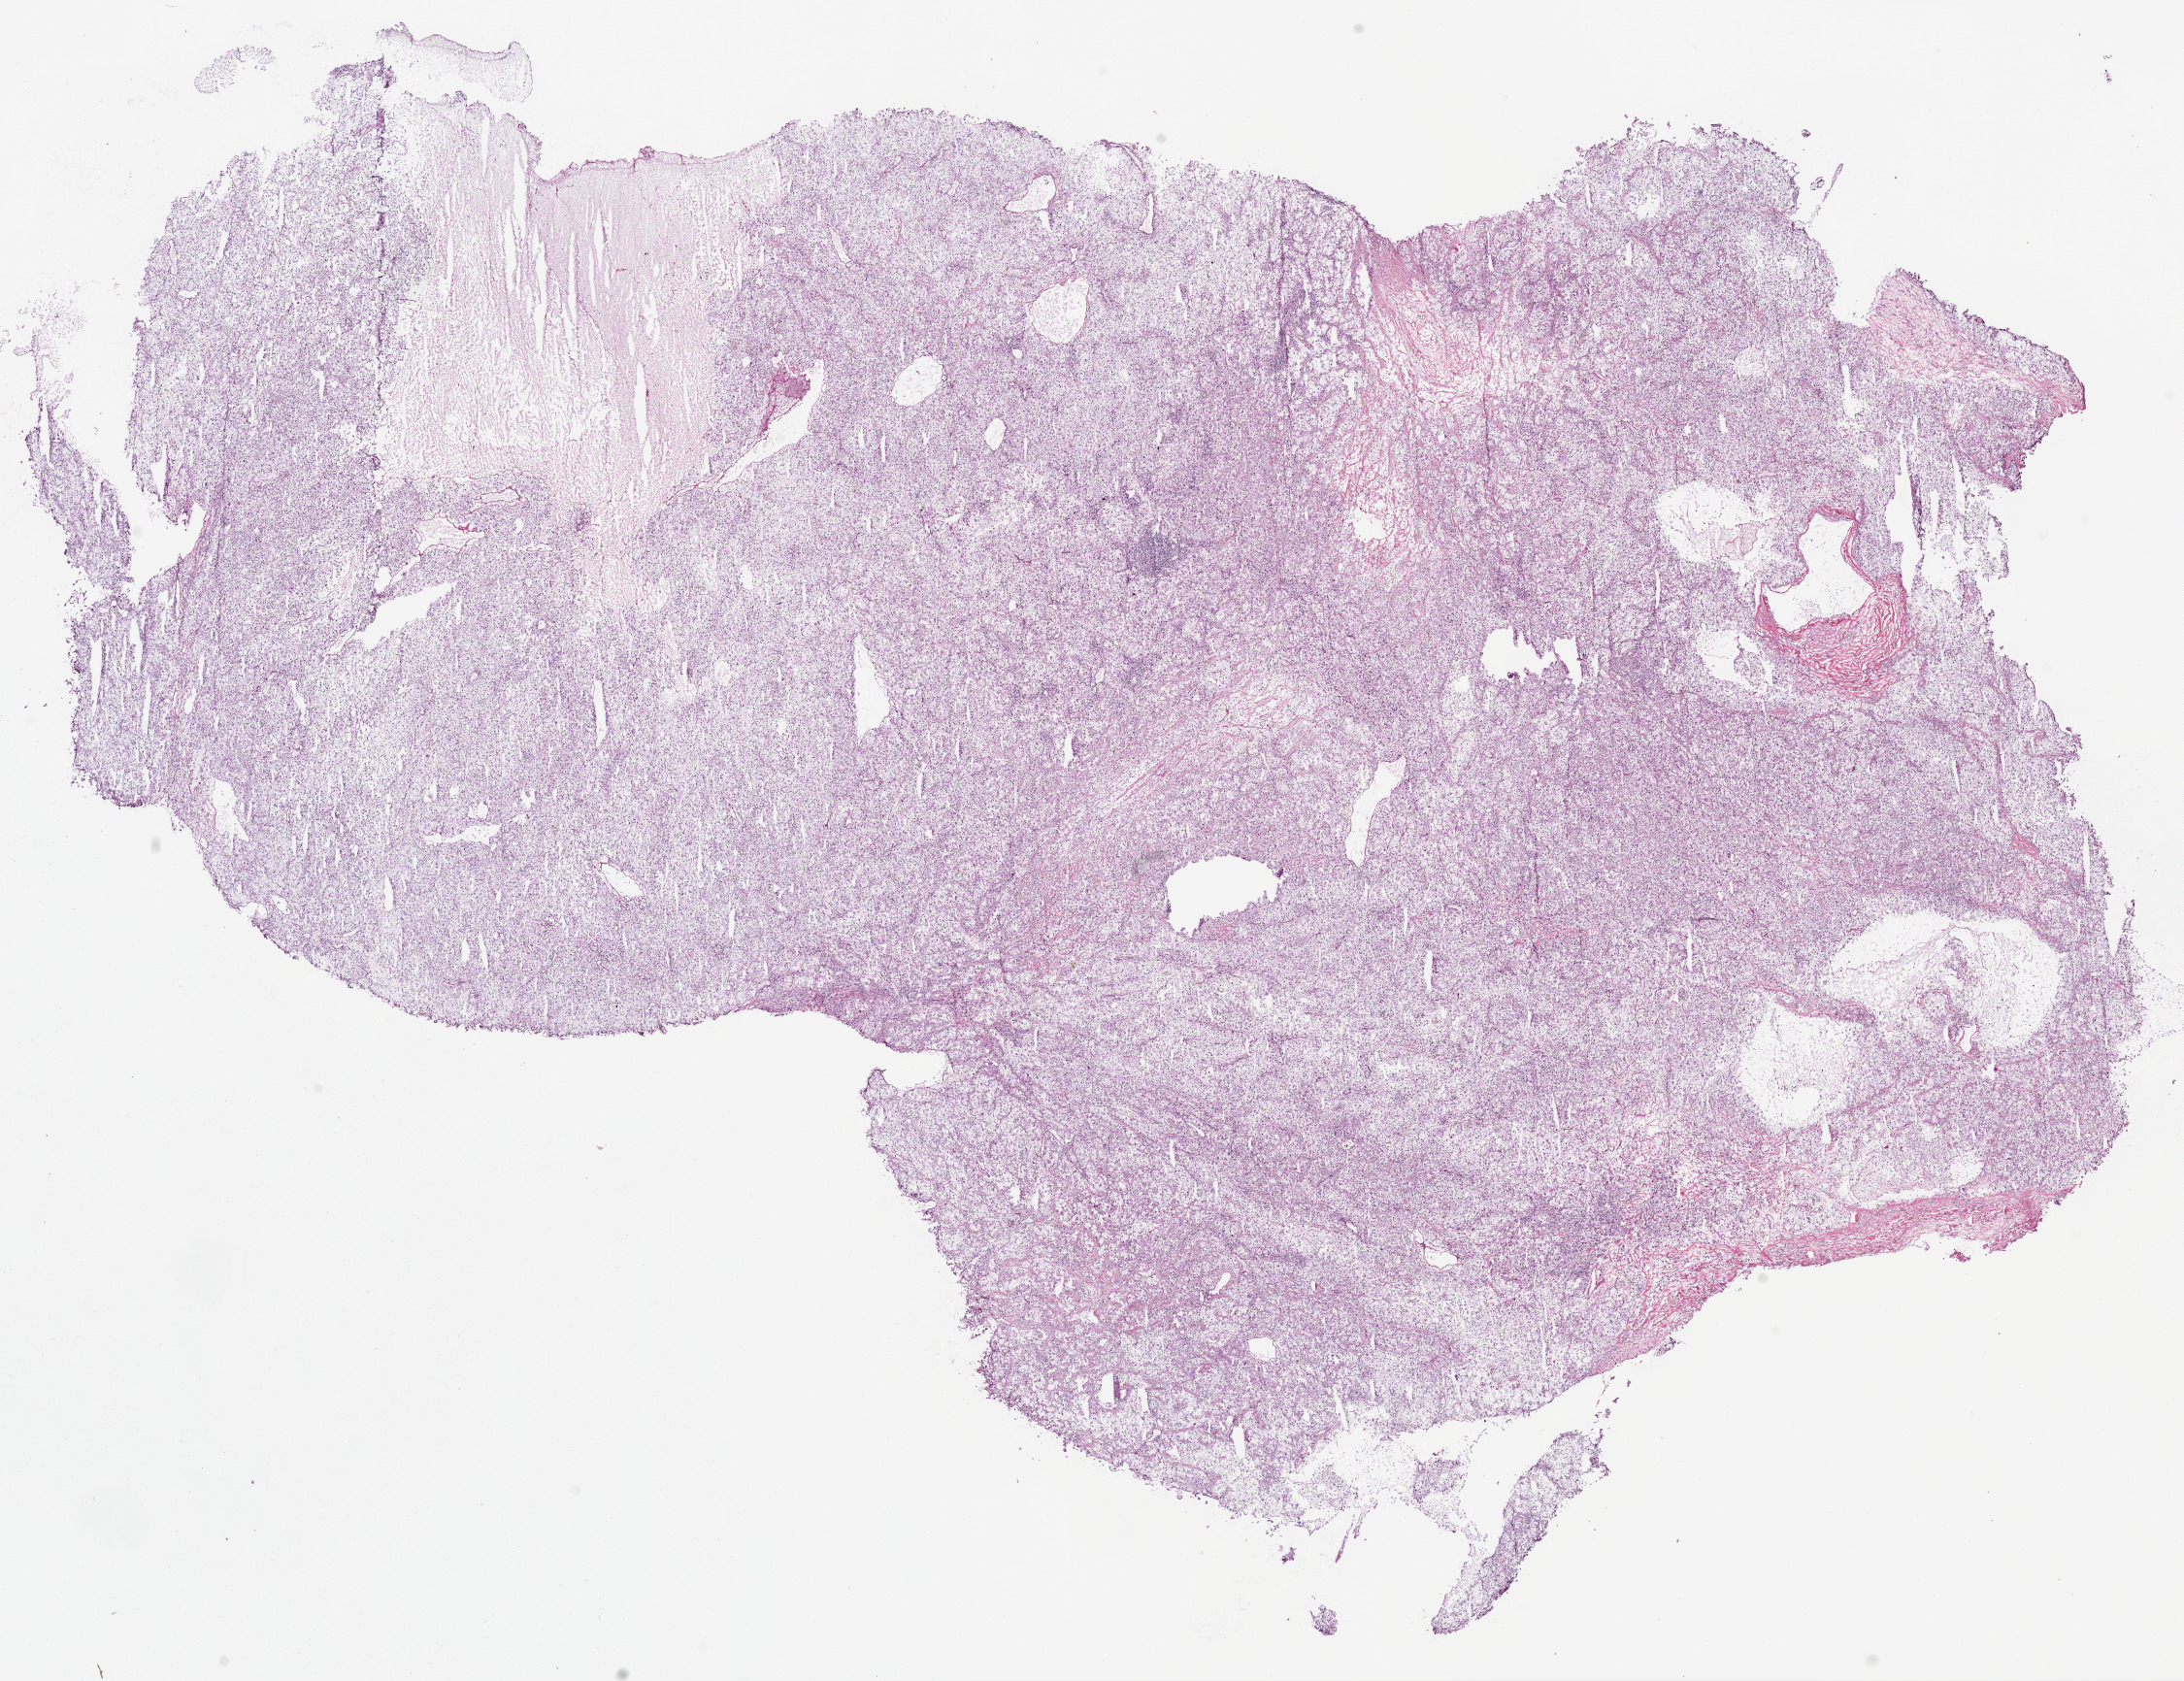
Digitized Hematoxylin and eosin (H&E) stained tissue section (whole slide), low-resolution overview of the scanned area, about 18.1 x 13.9 mm (acquisition: 20x scan). Frozen section. Primary tumour sample from the kidney. Patient: male, age at initial diagnosis 57 years. Histologic grade: G3 (poorly differentiated). Composition of this section per pathologist review: tumour cells 90%, tumour nuclei 85%, normal cells 0%, stromal cells 10%, necrosis 0%. Infiltration values recorded for this section: lymphocyte infiltration 5%, monocyte infiltration 2%, neutrophil infiltration 0%.
Histologic diagnosis: Clear cell adenocarcinoma, NOS. AJCC pathologic stage: II. Lymph nodes positive (case pathology): 0 of 7 examined. TNM: T2 N0 M0.